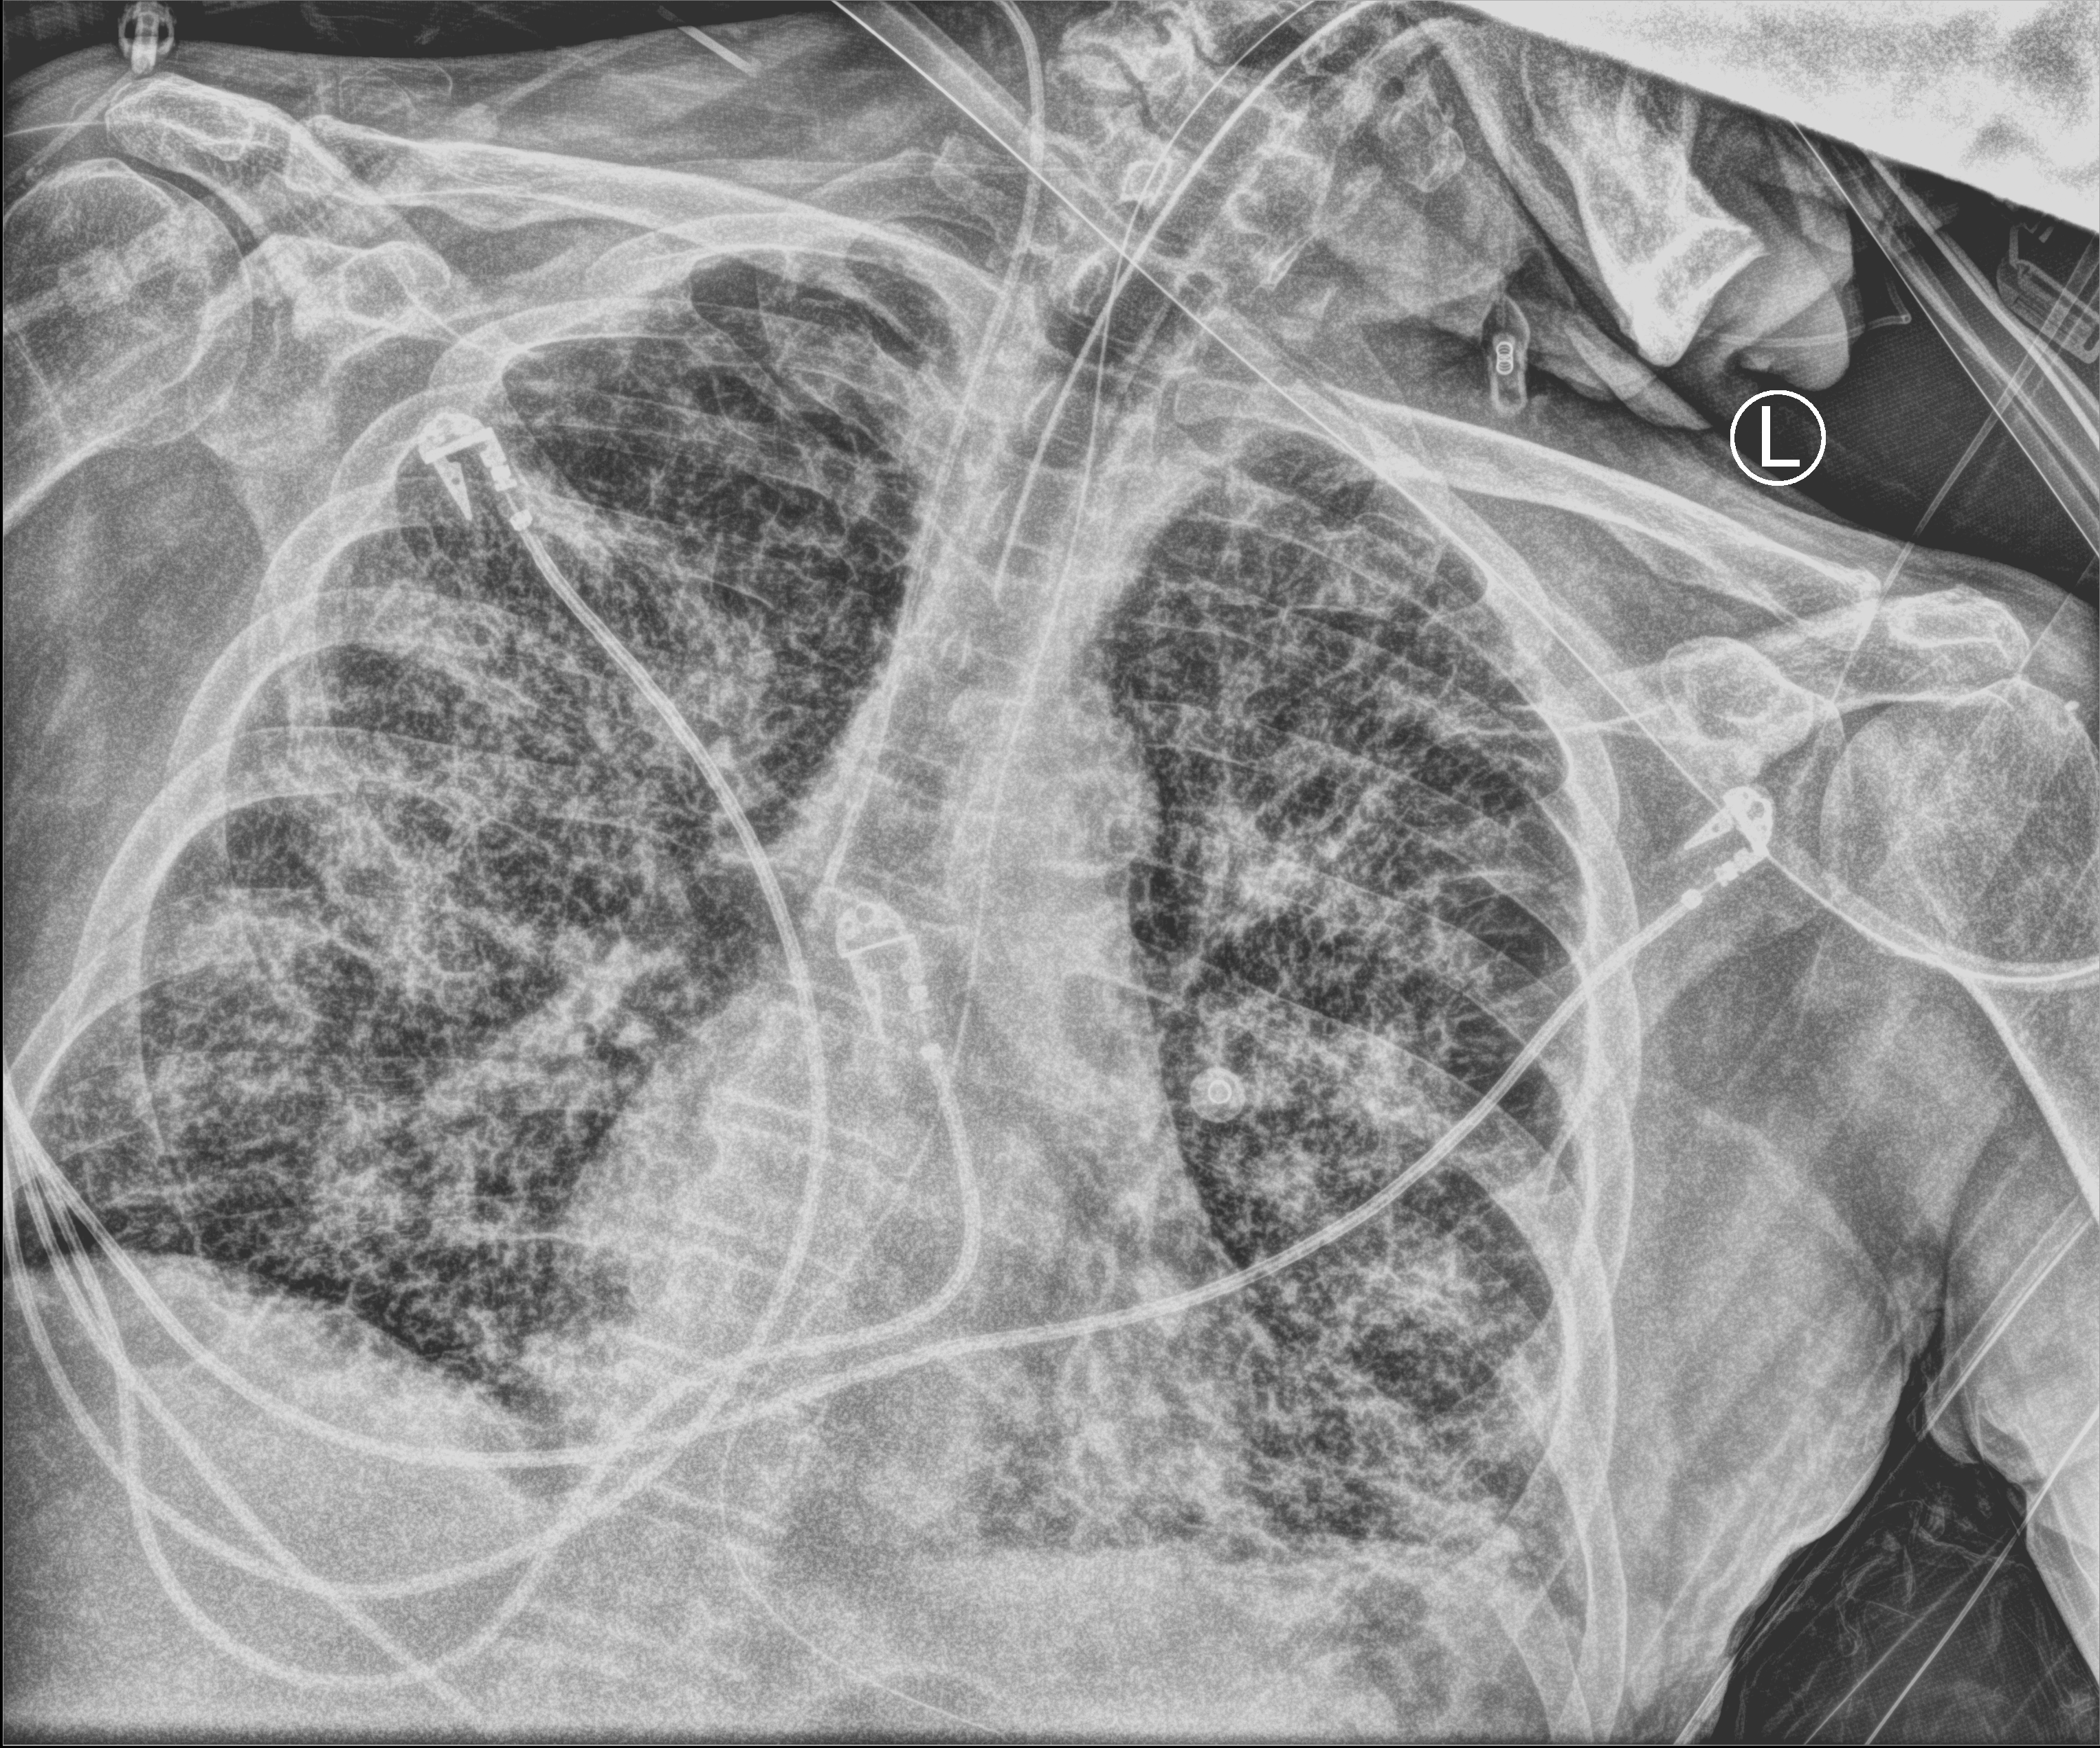
Portable chest radiograph; anteroposterior (AP) projection. Male patient hospitalised with COVID-19, age 75–90 years.
Admission-level facts for this patient (not findings on this image; timing relative to this image not recorded): admitted to intensive care during this hospital stay: yes; mechanically ventilated during this hospital stay: yes.